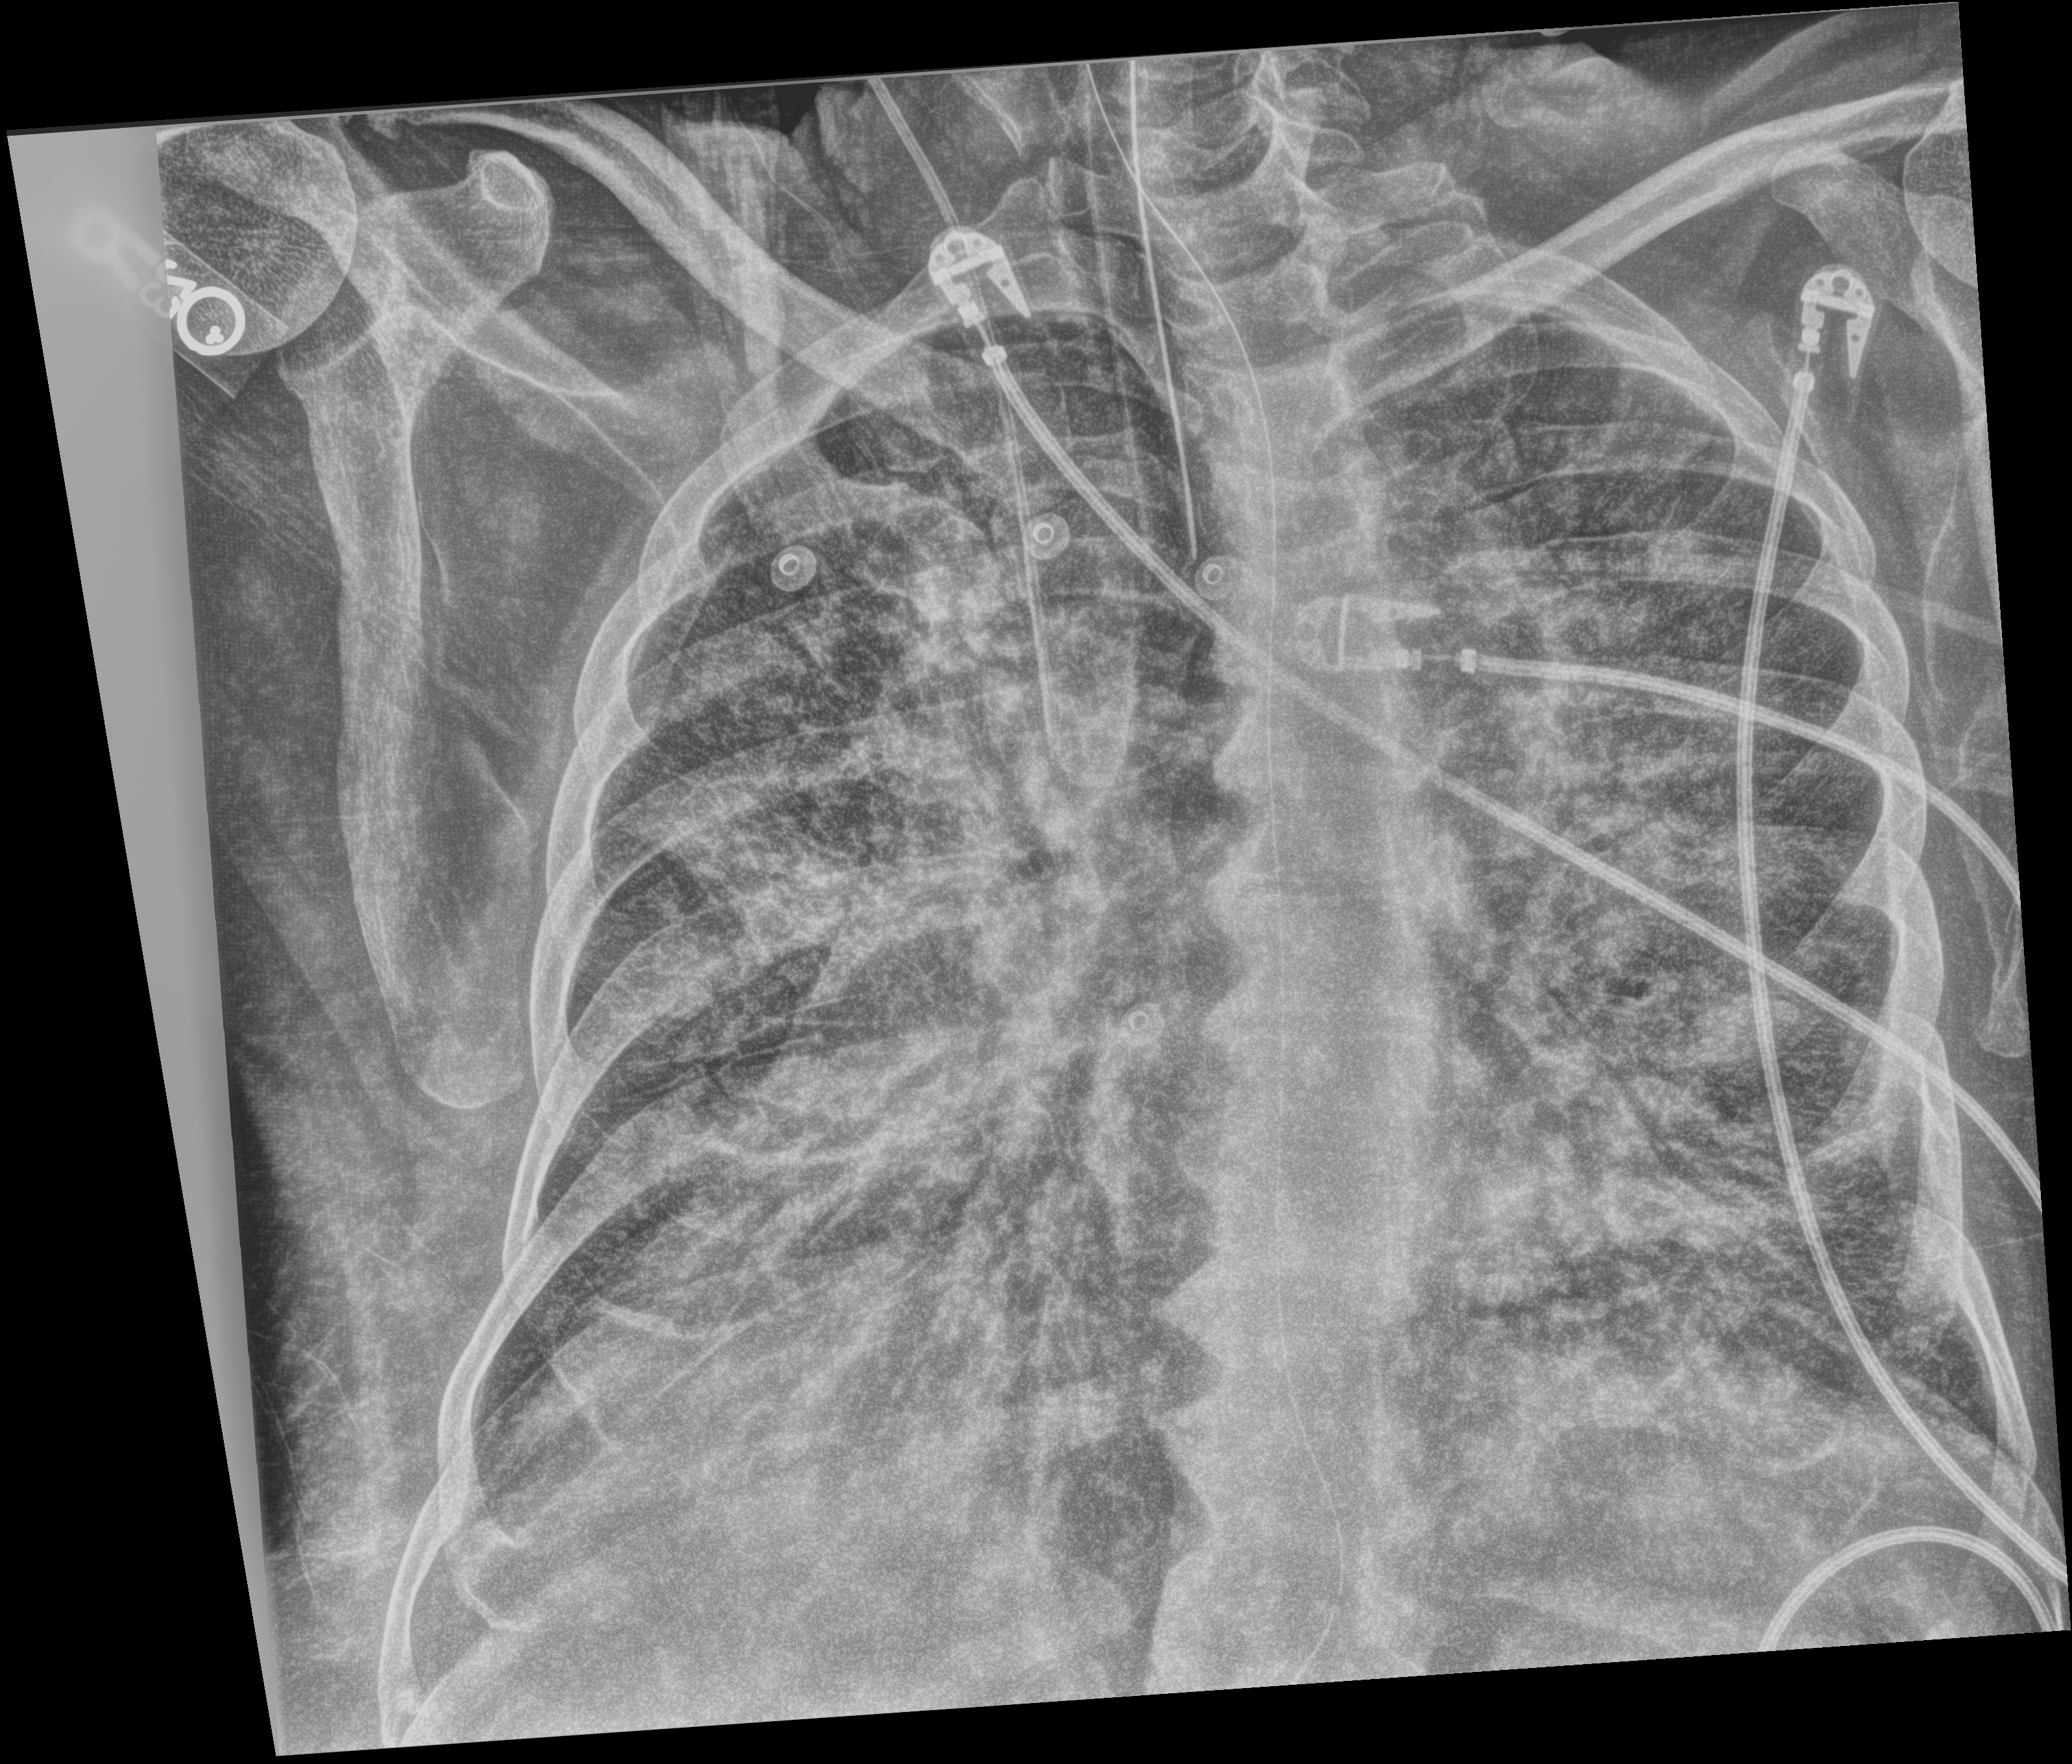
Chest X-ray (portable), anteroposterior (AP) projection. Male patient hospitalised with COVID-19, age 60–74 years.
Hospital-stay facts (about this admission, not read from this image; timing relative to this image not recorded): COPD (admission record): no.